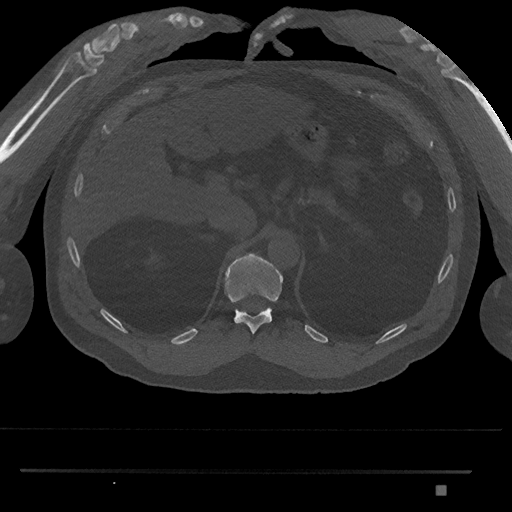
CT including the spine, one axial slice. Slice 939 of 1134 in the series (ordered by position). Reconstruction kernel Br40s/3. 120 kVp. Bone window (W 1800 / L 400 HU). 512 × 512 image matrix, field of view 429 × 429 mm. Male patient, age 65 years. Case-level facts recorded for this patient, not image findings: primary cancer: prostate.
Annotated regions visible in this slice (semi-automatically segmented with operator editing):
- T11 vertebra: box from (x=224, y=253) to (x=284, y=334) px